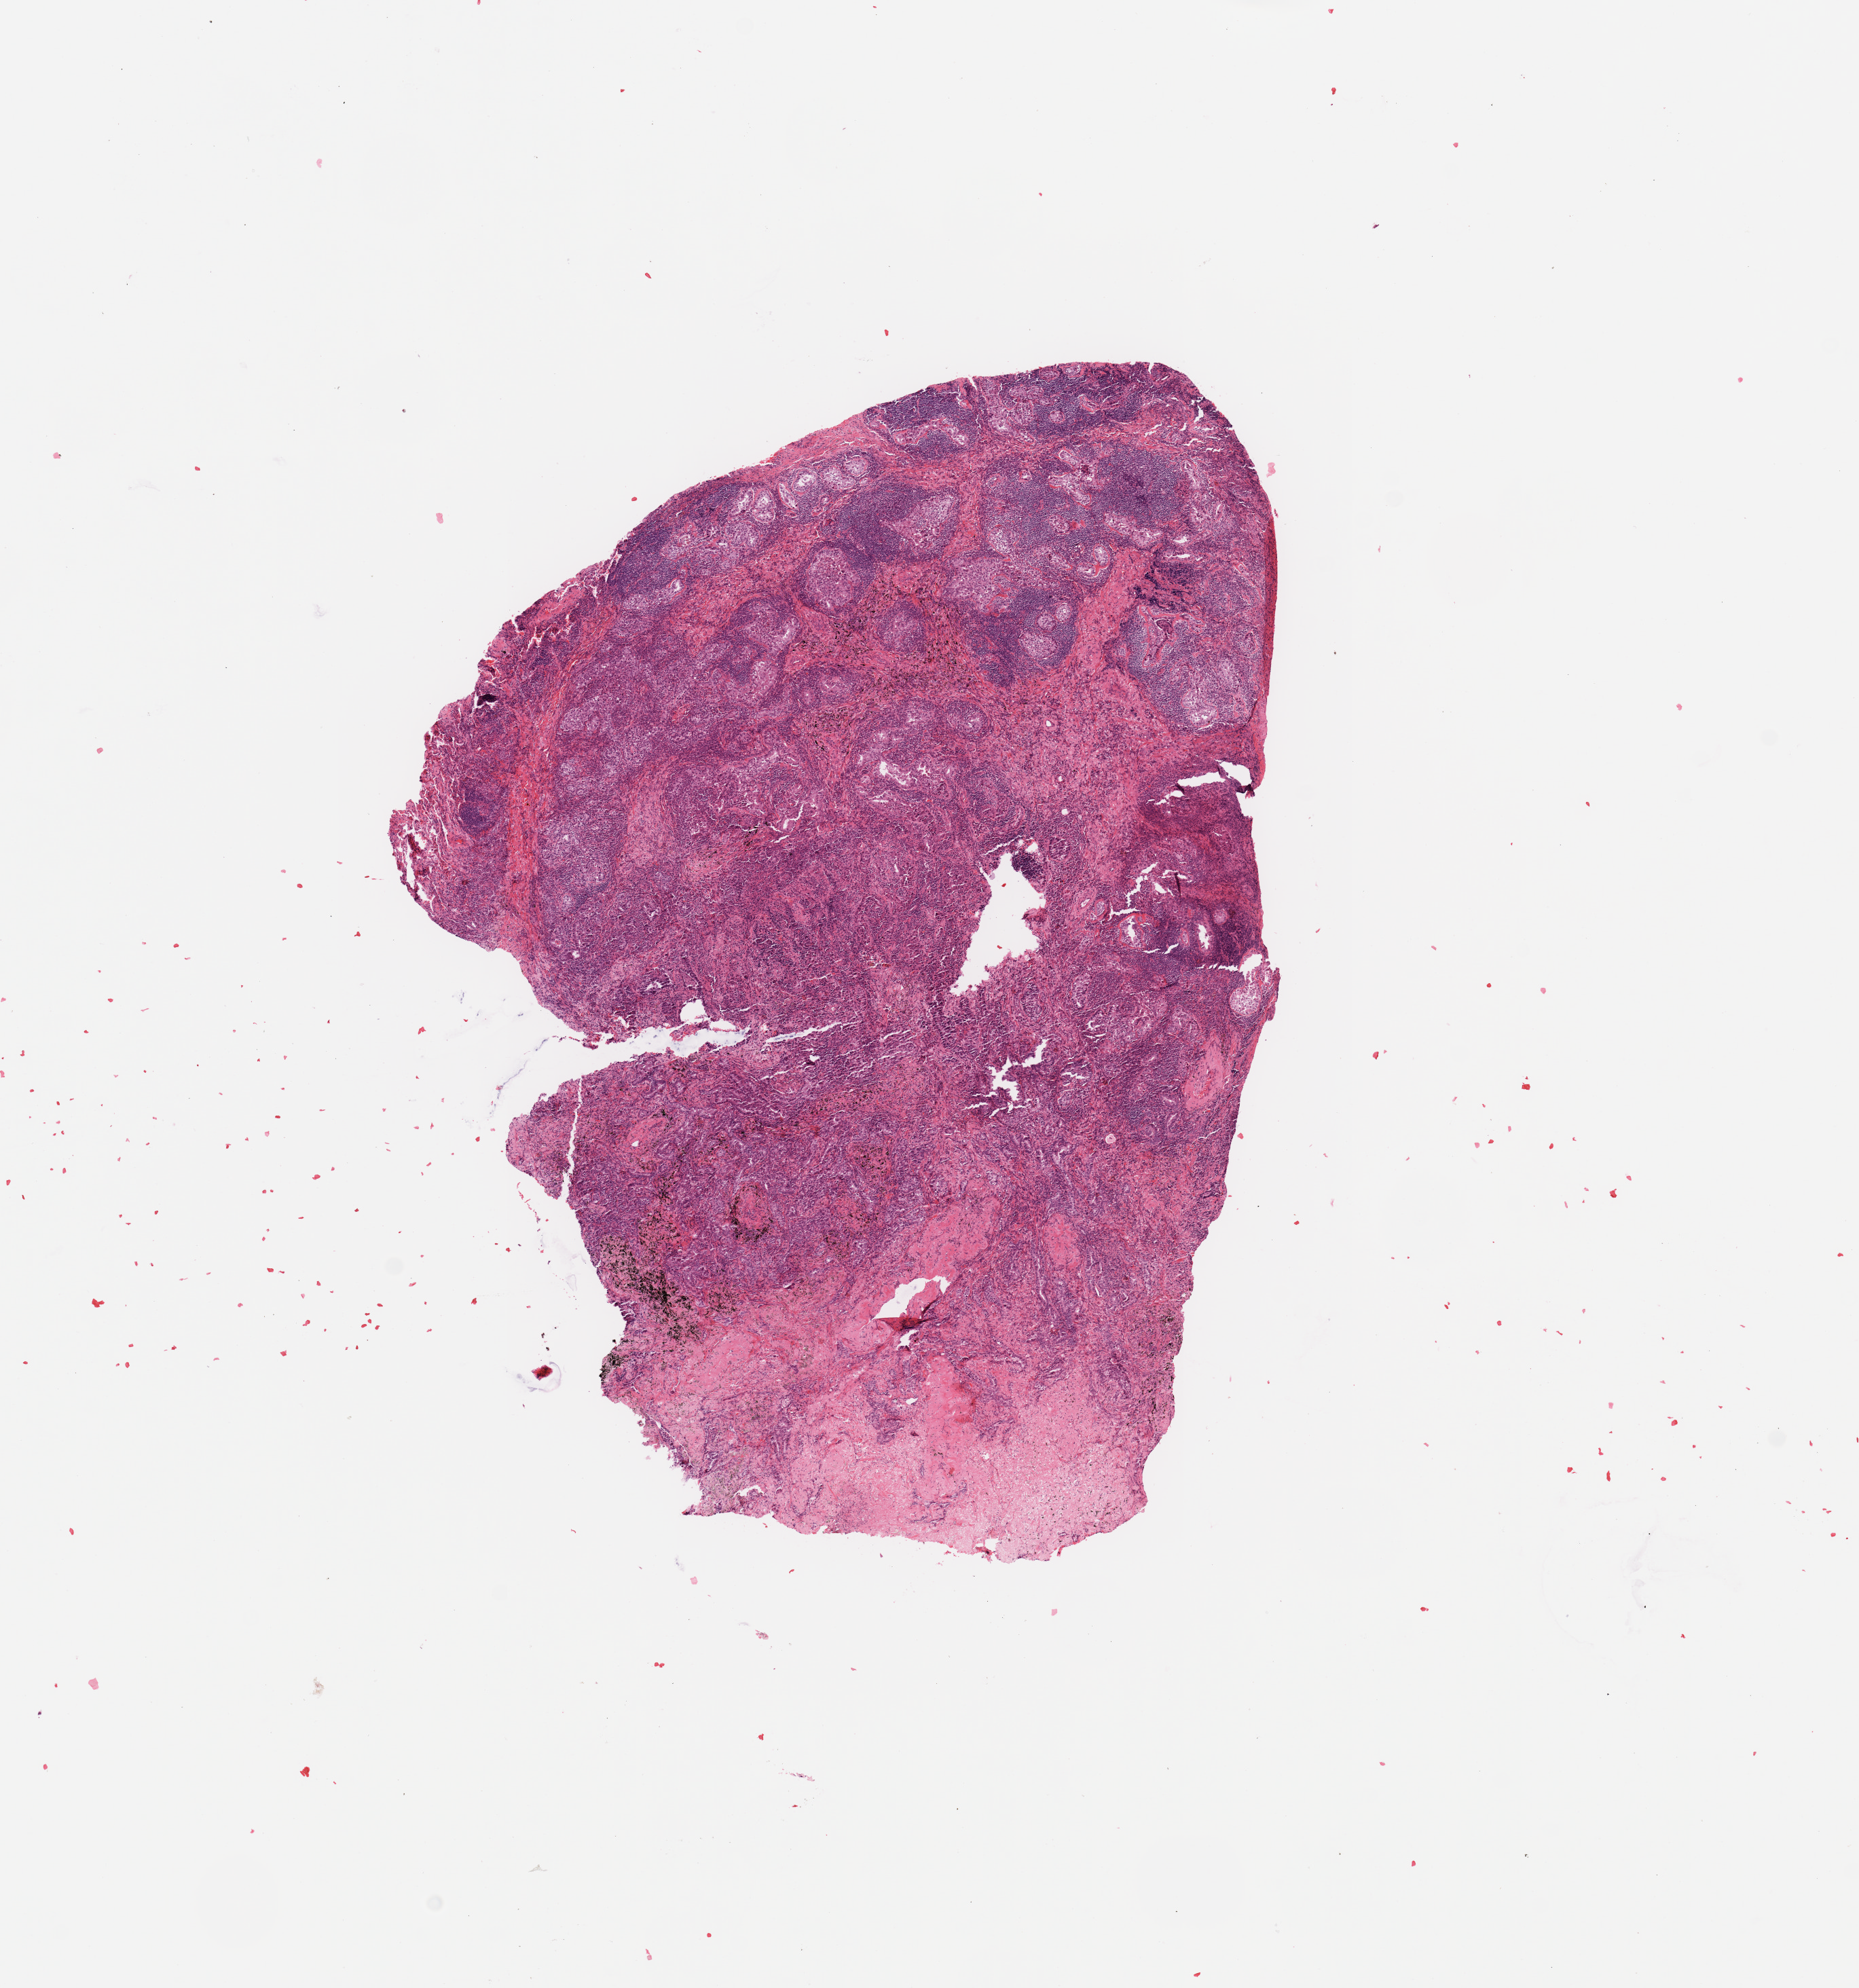
Whole-slide histology image, H&E-stained, a low-resolution overview of the entire scanned area, about 10.8 x 11.6 mm. Tumour tissue sample, sampled site: lung. Male, 68 y/o. Histologic grade: G2 (moderately differentiated). Composition of this section per pathologist review: tumour nuclei 70%, necrosis 5%.
- AJCC pathologic stage: IA2
- diagnosis: Adenocarcinoma, NOS
- primary tumour site (as recorded): right upper lobe